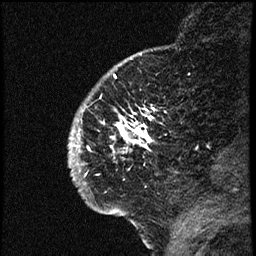
Breast MRI (dynamic contrast-enhanced), one sagittal slice; position 14 of 66 along the scan axis; dynamic contrast-enhanced study with each time point stored as its own series, time point 2 of 3 at this slice position (early post-contrast, ordered by acquisition time); 1.5 T; TE 4.2 ms, TR 17.6 ms; 2 mm slice thickness; 256 × 256 image matrix. Female patient. From the clinical record (not read from this slice): setting: breast cancer imaged before/during neoadjuvant chemotherapy; receptor status: HER2-positive.
Annotated regions visible in this slice (semi-automatically segmented with operator editing):
- analysis volume of interest (the breast-tissue region the enhancement analysis was run in; not a lesion): bounding box (x1, y1, x2, y2) in pixels: (71, 69, 177, 209)
- tumour enhancement mask (voxels above the 100 % enhancement threshold inside the analysis volume of interest): (73, 109, 155, 171)